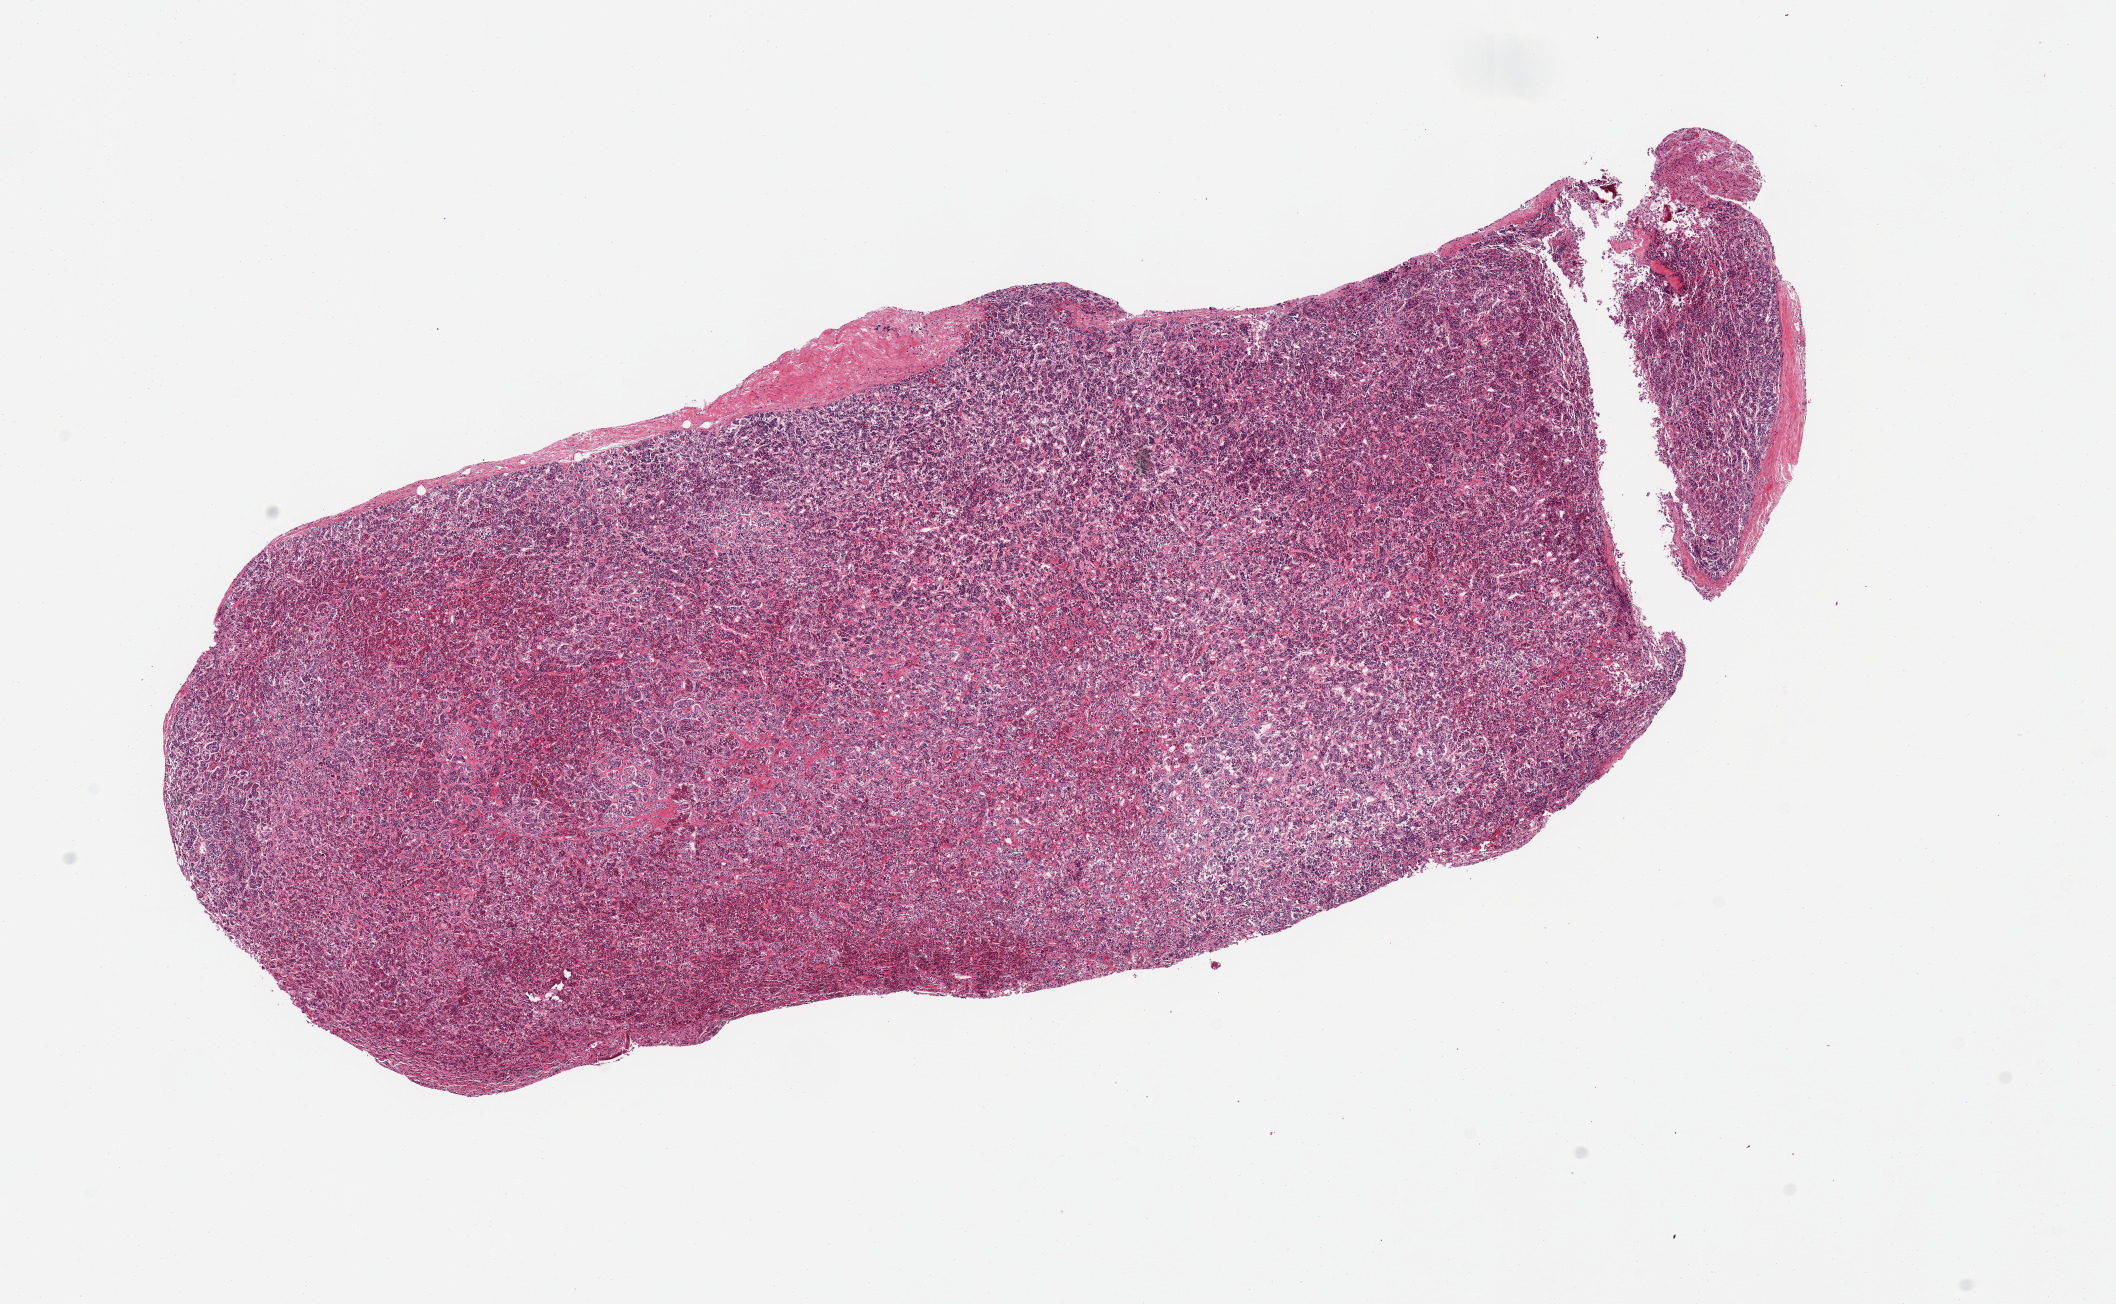
Digitized hematoxylin and eosin (H&E)-stained section — shown as a low-resolution overview of the whole scanned area (about 16.7 x 10.3 mm). PAXgene-fixed, paraffin-embedded tissue. Sampled site (target tissue): pituitary. Tissue donor sample. Donor sex: male.
Pathologist's review note for this sample: 1 piece, all adenohypophysis.